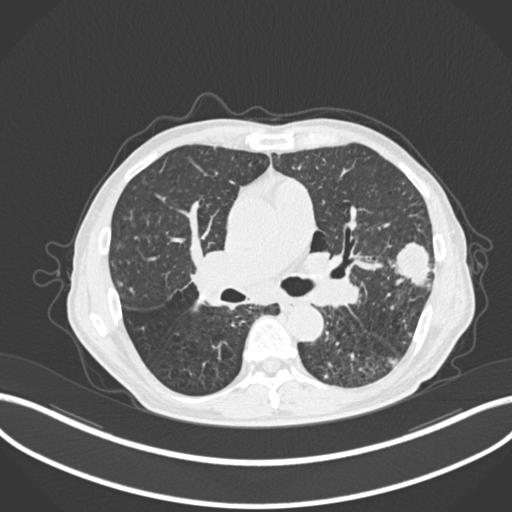
Chest CT, one axial slice; position 138 of 287 along the scan axis; reconstruction kernel B30f; 120 kVp; lung window (W 1500 / L -600 HU); 1 mm slice thickness; 512 × 512 image matrix. Patient: male, 74 years. Case-level facts recorded for this patient, not image findings: clinical TNM (as recorded): T2a N1 M0.
Annotated regions visible in this slice (bounding box drawn by a radiologist):
- lung tumour (recorded histology: adenocarcinoma): bounding box [x1, y1, x2, y2] px = [393, 239, 431, 292]